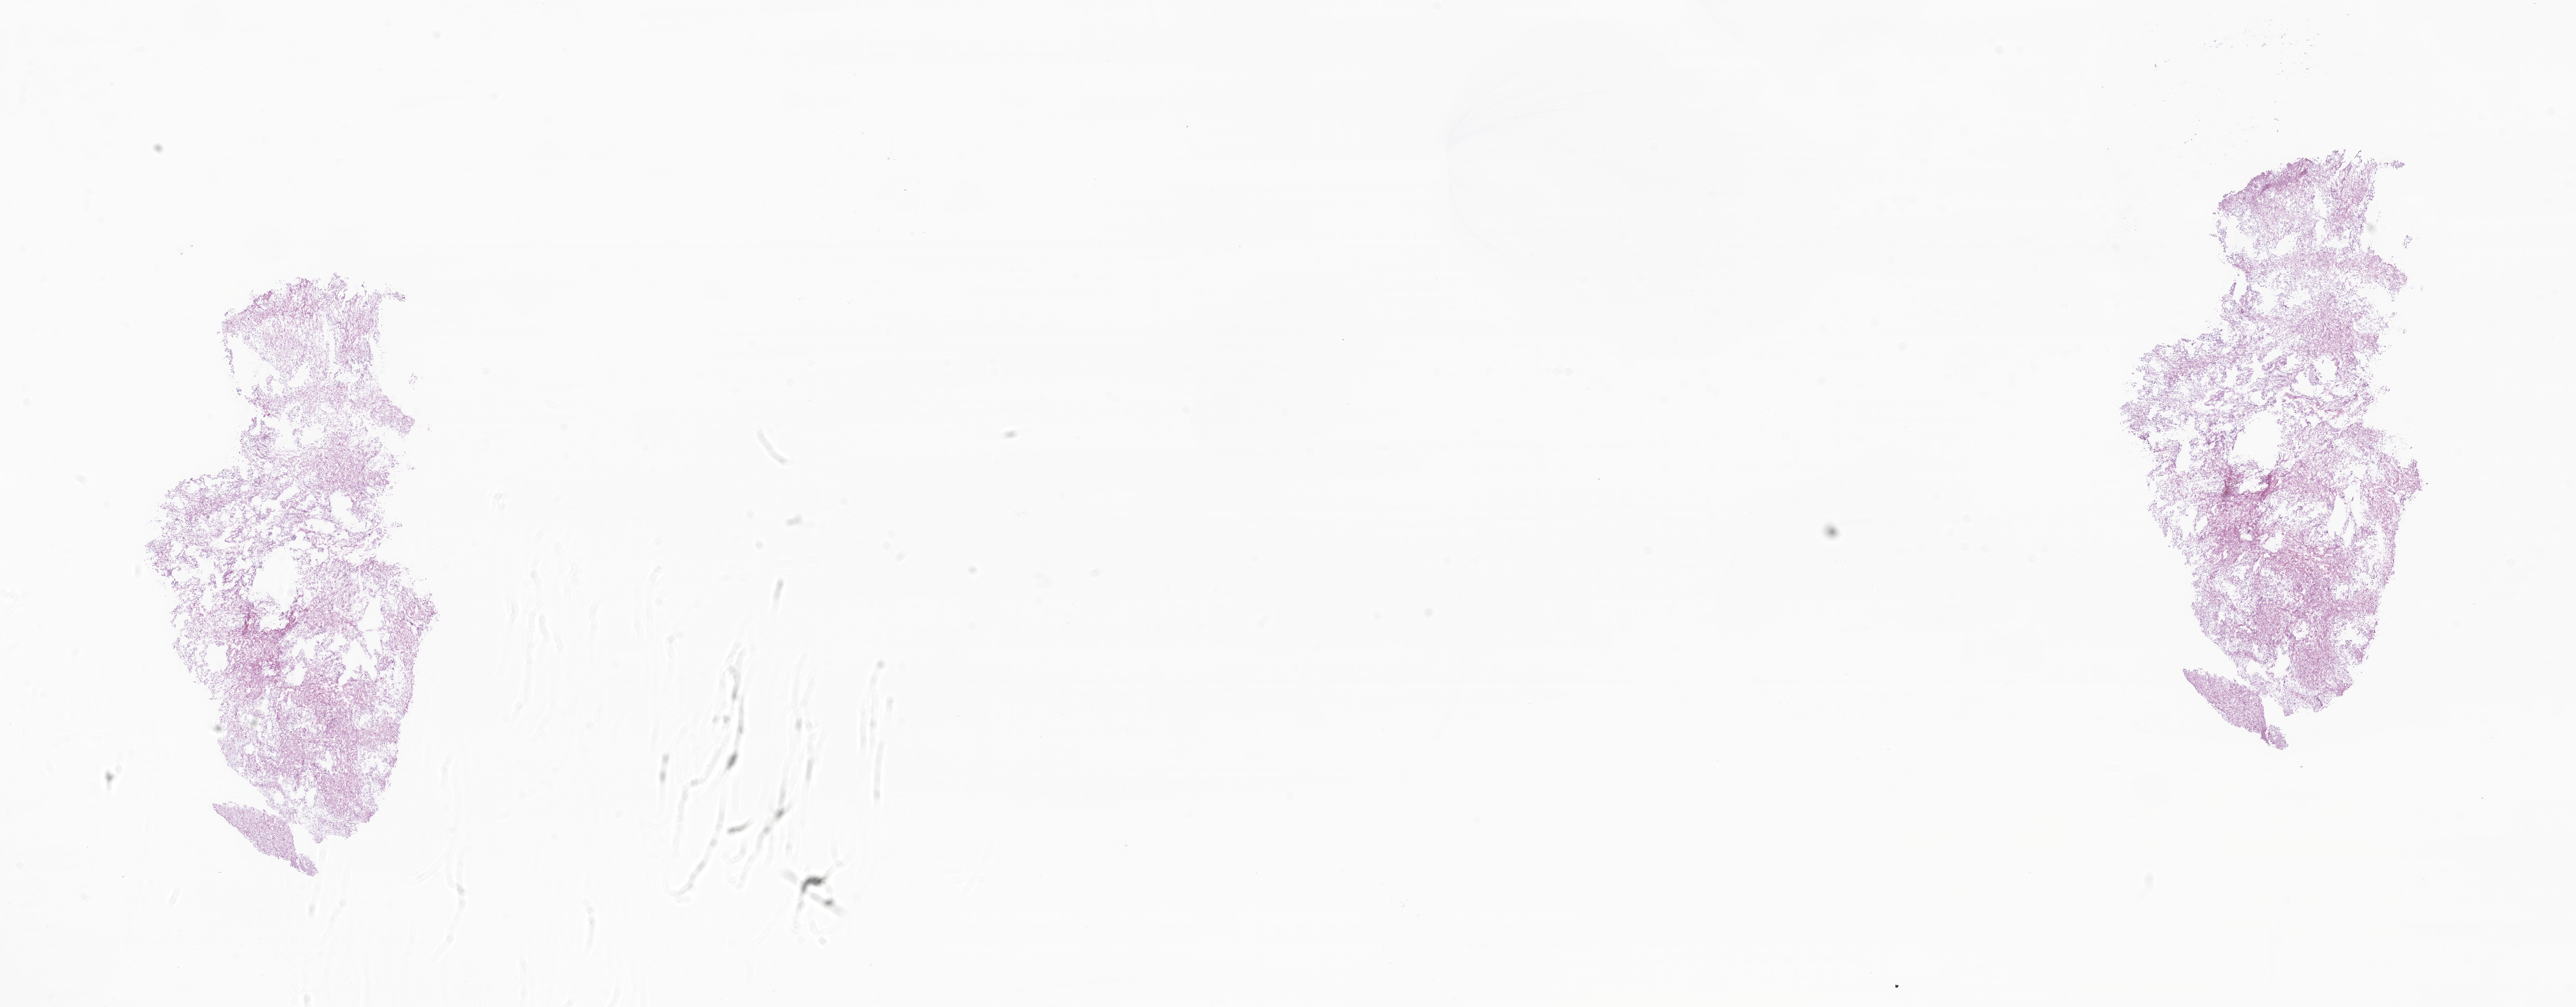
Digitized hematoxylin and eosin (H&E)-stained section of tumor tissue from the brain — shown as a low-resolution overview of the whole scanned area (about 31.6 x 12.3 mm); frozen section (OCT-embedded). Patient female; age 127 months (10 years 7 months).
Diagnosis: Glioma, malignant.